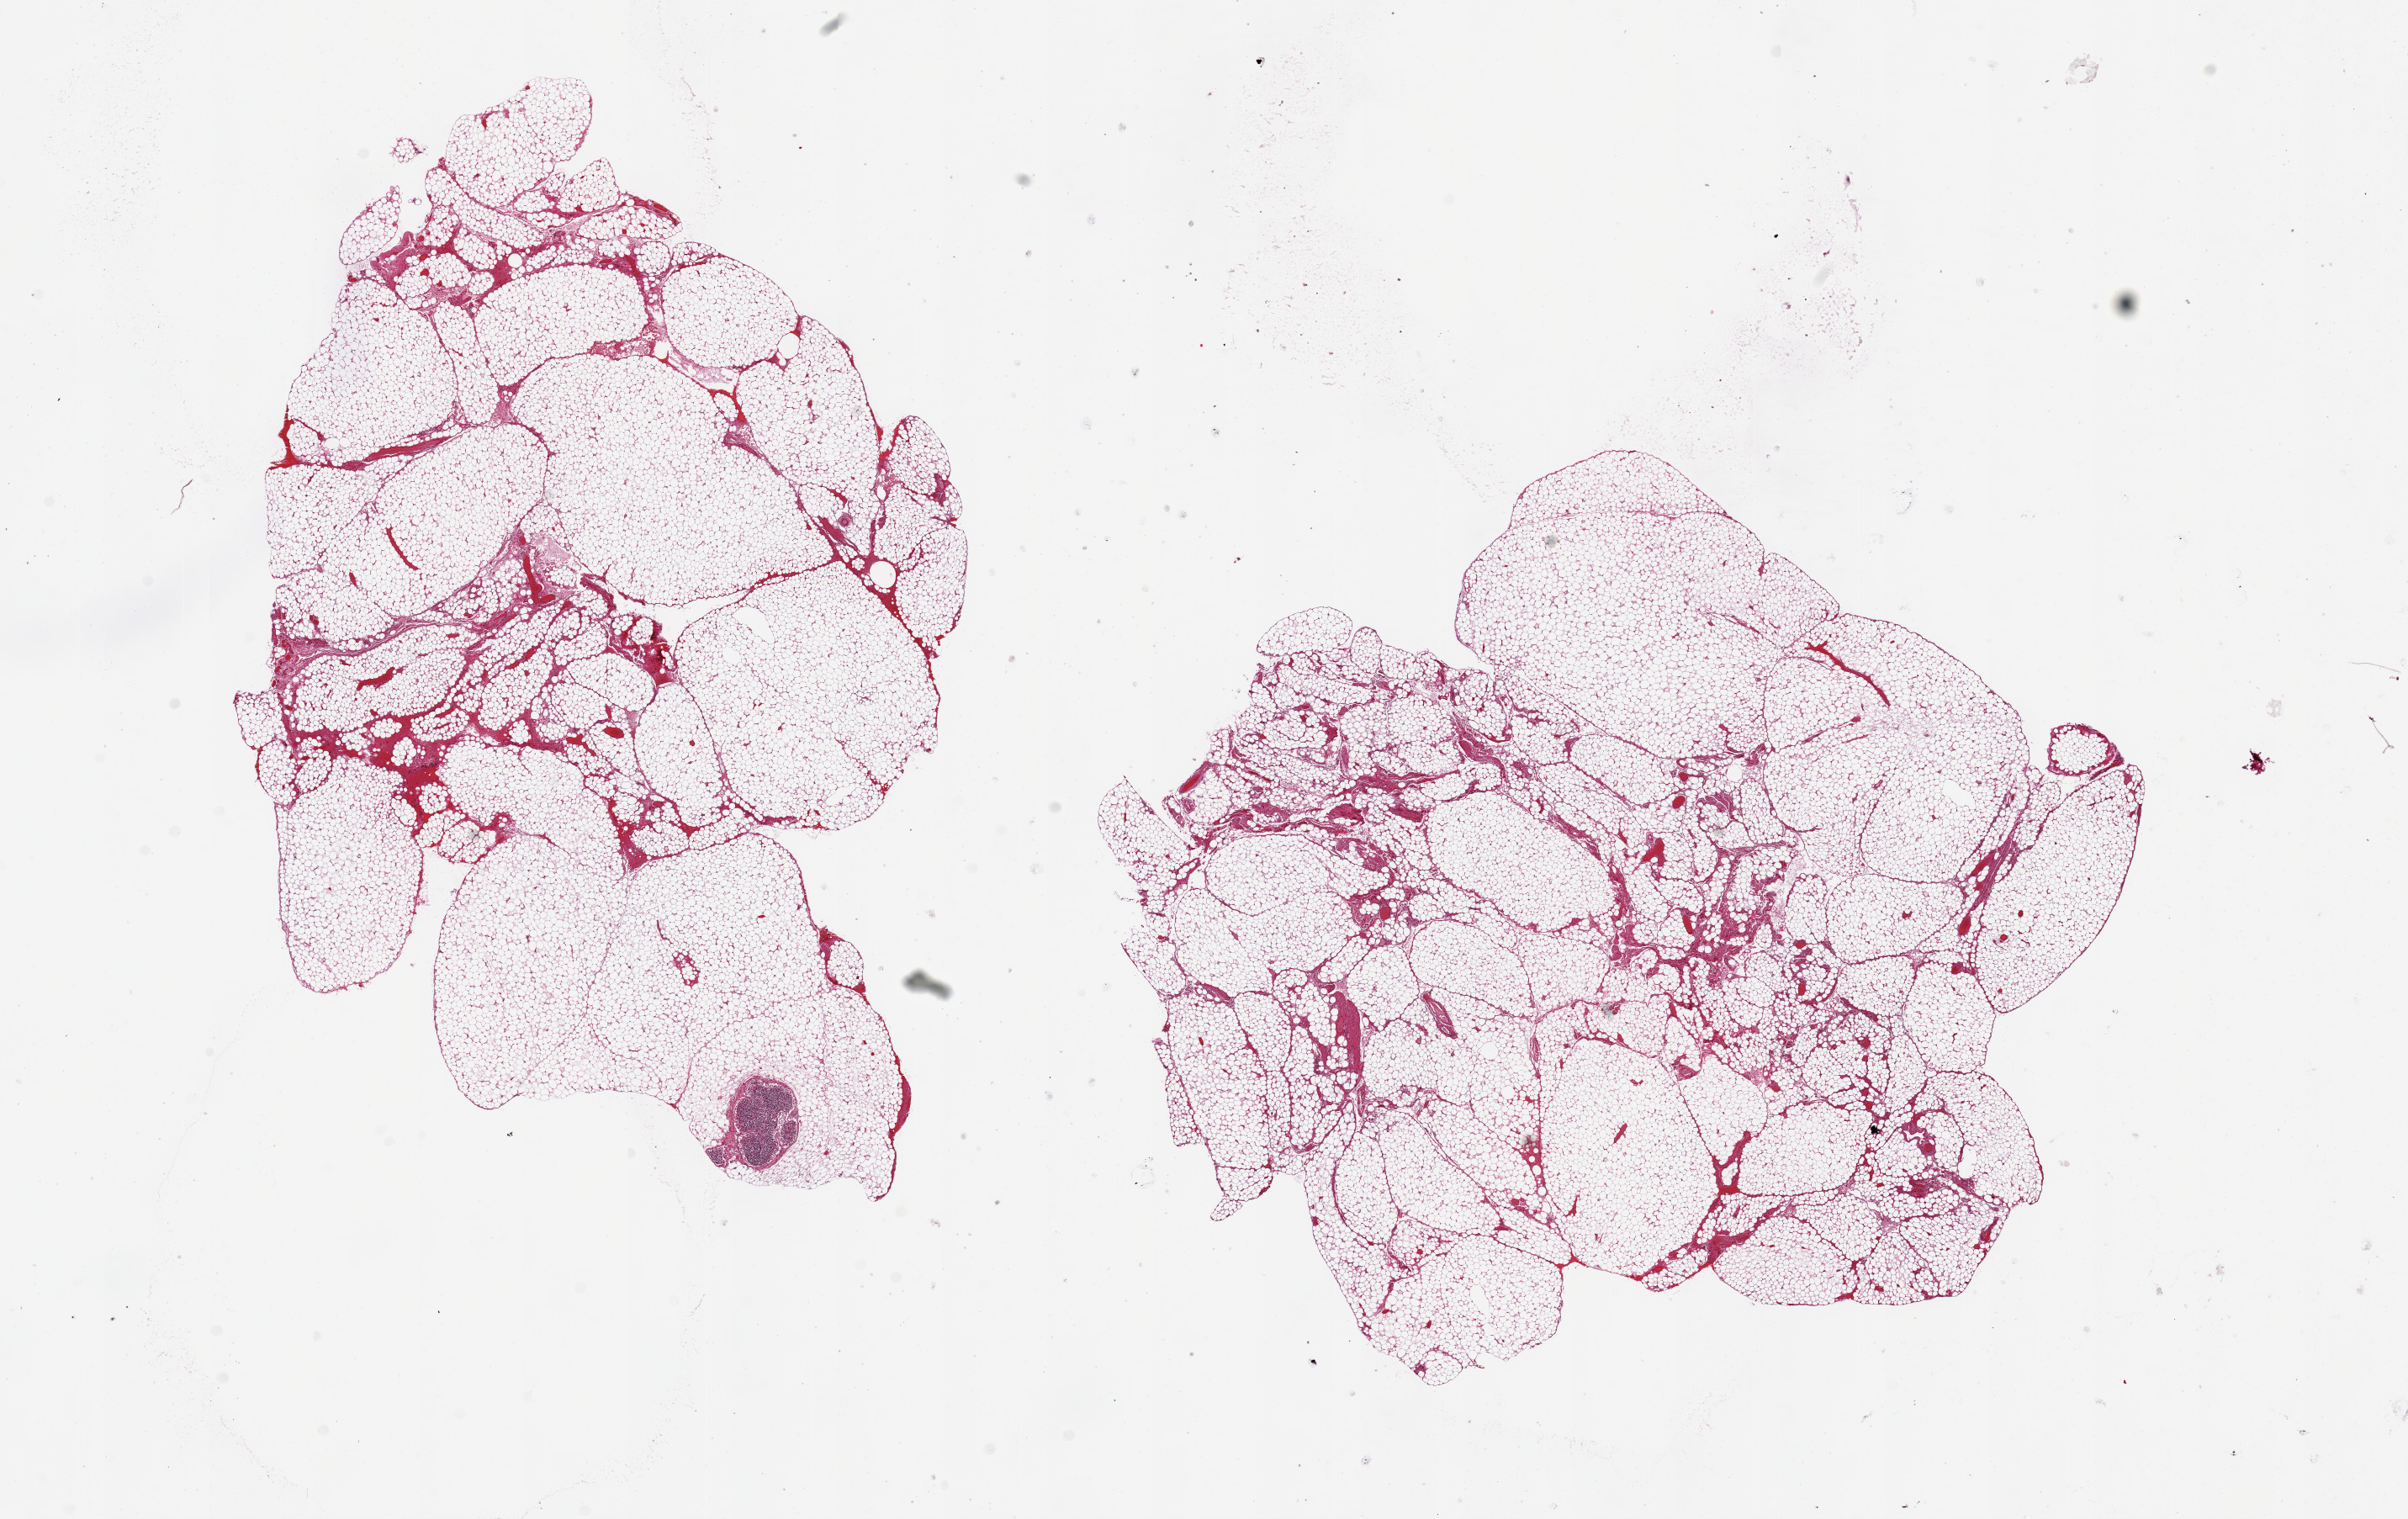
H&E whole-slide image, whole scanned area (about 22.6 x 14.3 mm, slide scanned at 20x) shown as a low-resolution overview, PAXgene-fixed paraffin-embedded (PFPE) section, sampled site (target tissue): omentum, donor tissue sample. Donor sex: male.
Pathologist's review note for this sample: 2 pieces, 11x7 & 10x9mm; incidental 05mm lymph node present.